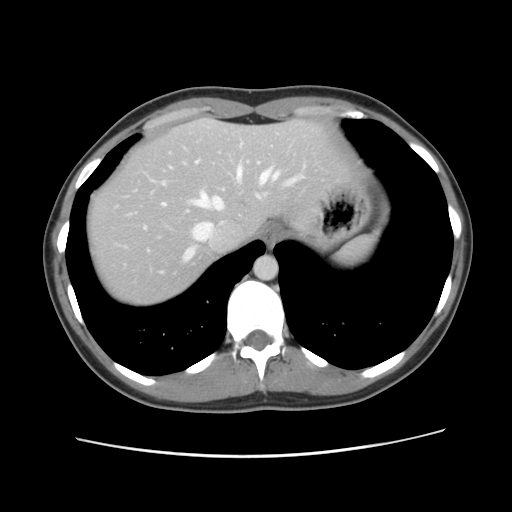
Contrast-enhanced abdominal CT, one axial slice; position 100 of 134 along the scan axis; 120 kVp; intravenous contrast given; soft-tissue window (W 400 / L 40 HU); 2.5 mm slice thickness; 512 × 512 image matrix. Female patient, age 33 years. From the clinical record (not read from this slice): diagnosis: colorectal cancer liver metastases, imaged before liver resection; multiple liver metastases: yes; largest metastasis: 4.5 cm; chemotherapy before resection: no.
Structures marked on this image (expert manual segmentation):
- hepatic veins: bounding box <161,160,303,260> (left, top, right, bottom; pixels)
- liver: <86,119,347,307>
- planned liver remnant (the part of the liver to remain after resection): <86,119,347,307>
- portal vein (with intrahepatic branches): <116,206,149,250>